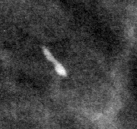
Crop from a digitized film mammogram around one marked abnormality, left breast, MLO view, BI-RADS breast density category 1 (scale 1–4).
- Marked abnormality: calcifications, distribution regional; BI-RADS assessment category 2; benign without callback (not worked up further).